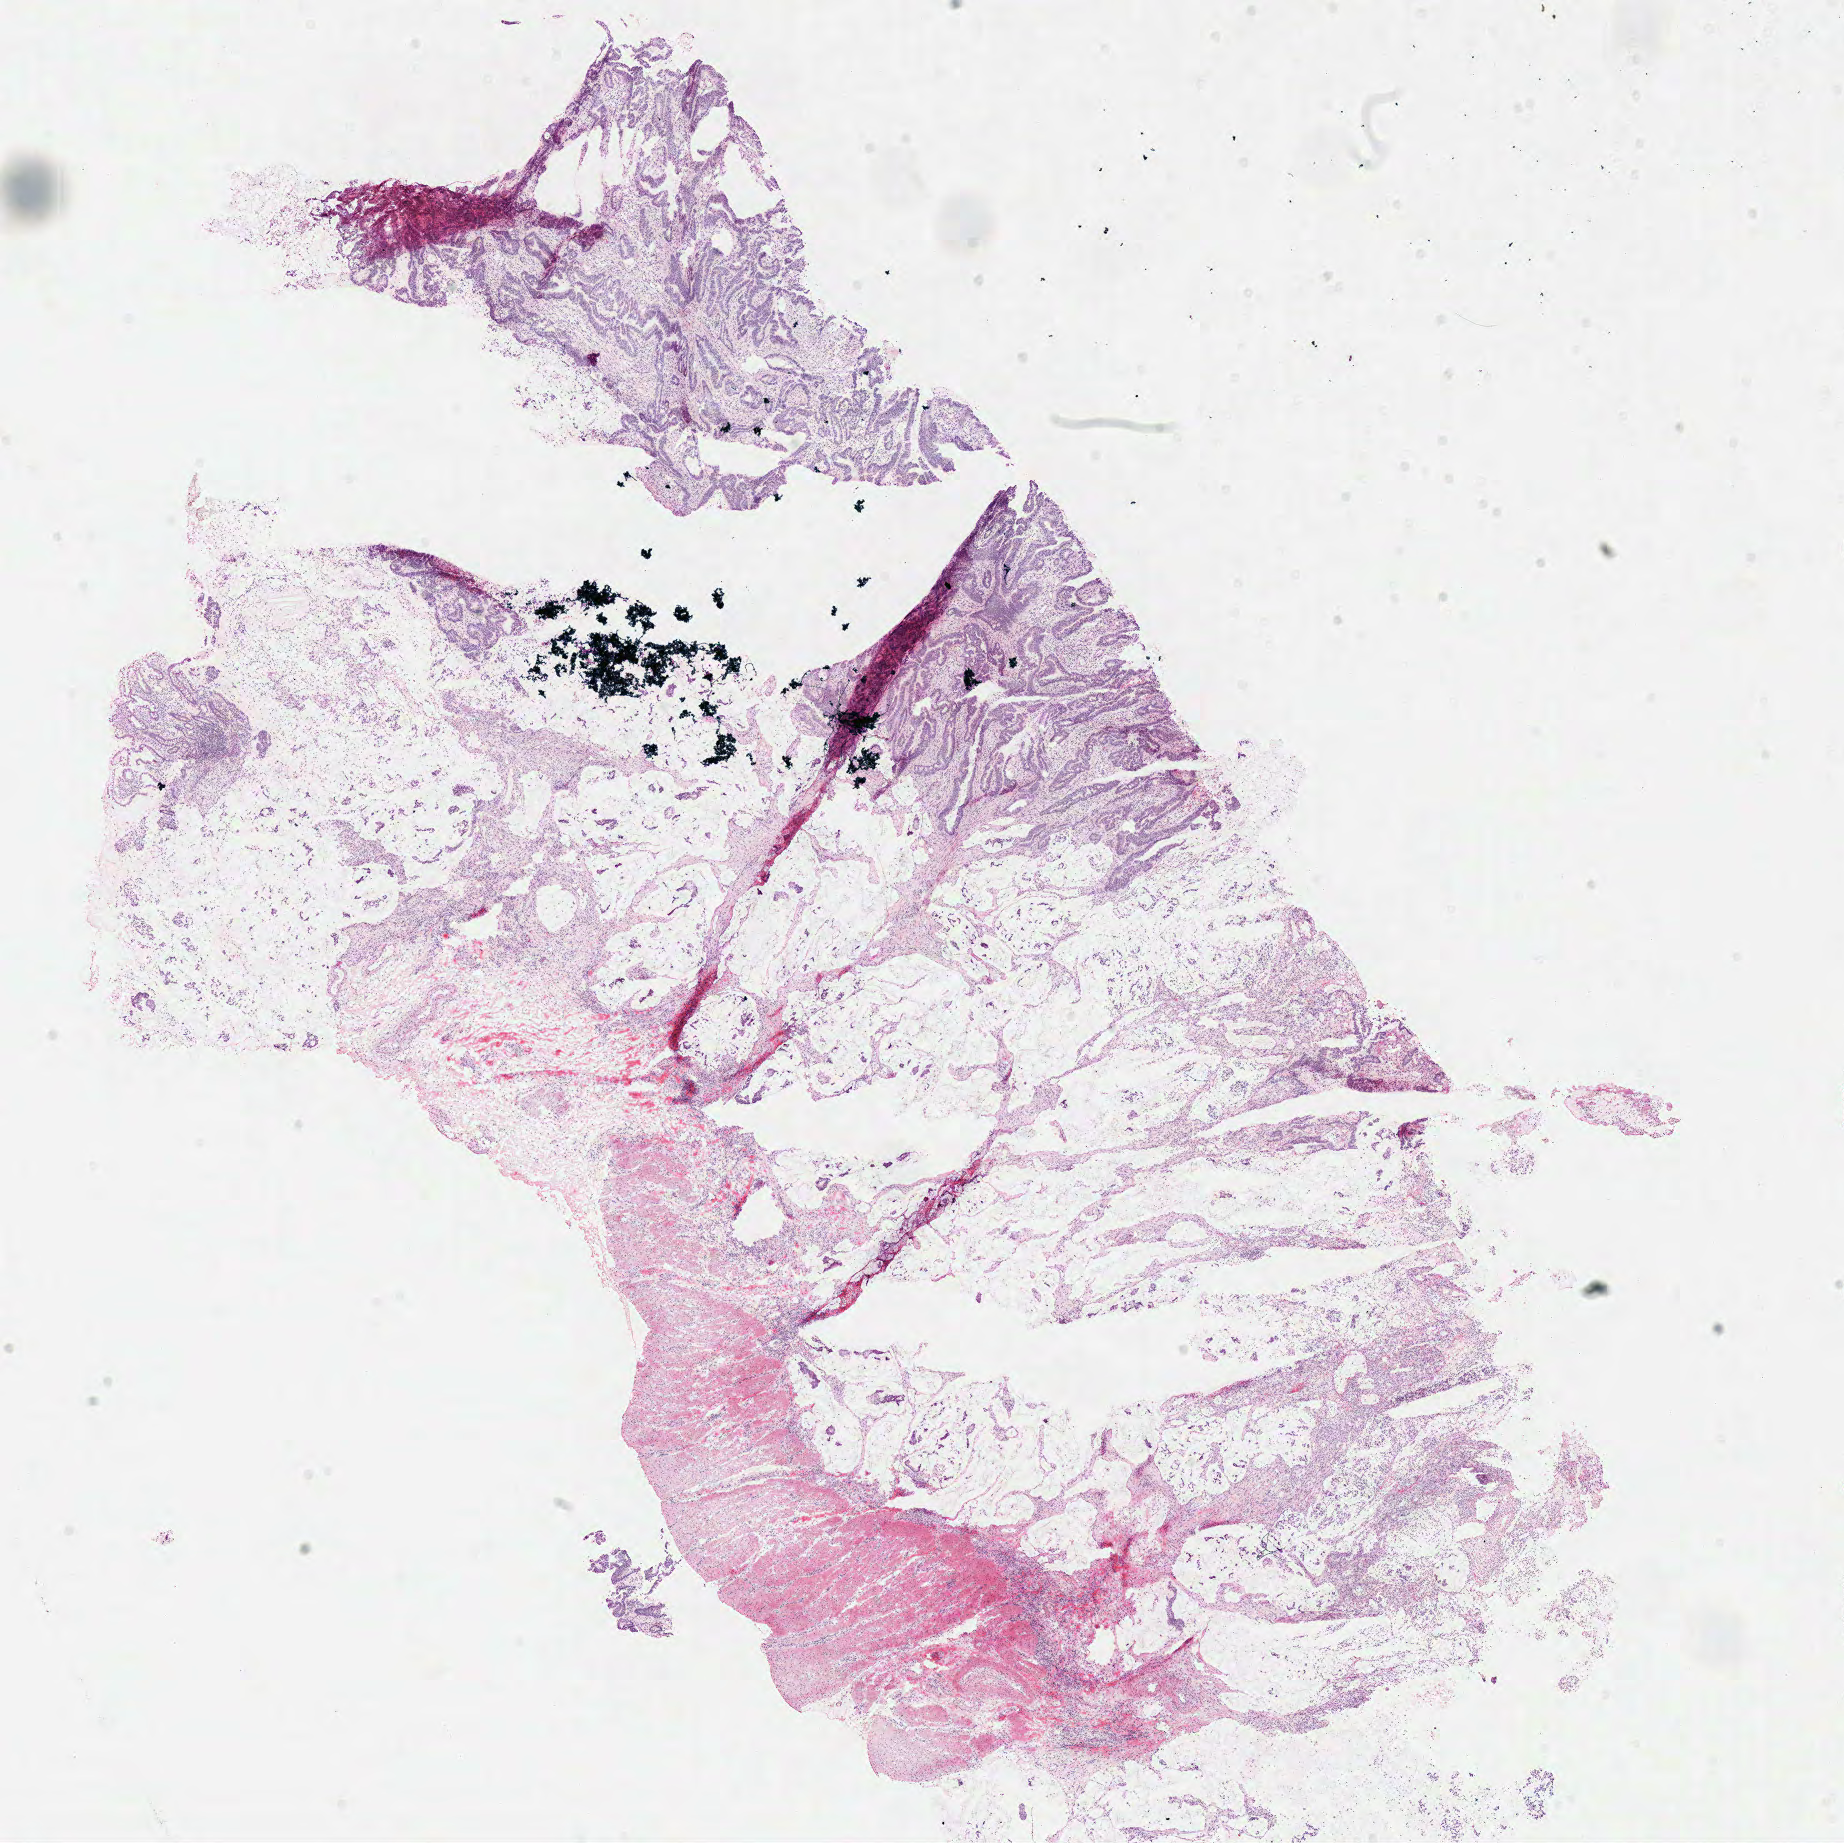
H&E whole-slide image — low-resolution overview of the scanned area, about 14.5 x 14.5 mm (slide scanned at 40x). Frozen section from the top of the tissue portion. Colon, primary tumour sample. Female, age 48 years at initial diagnosis. Composition of this section per pathologist review: tumour cells 71%, tumour nuclei 75%, normal cells 3%, stromal cells 15%, necrosis 1%.
Diagnosis: Mucinous adenocarcinoma (ascending colon). AJCC pathologic stage: IIIB. Lymph nodes positive (case pathology): 1 of 46 examined.